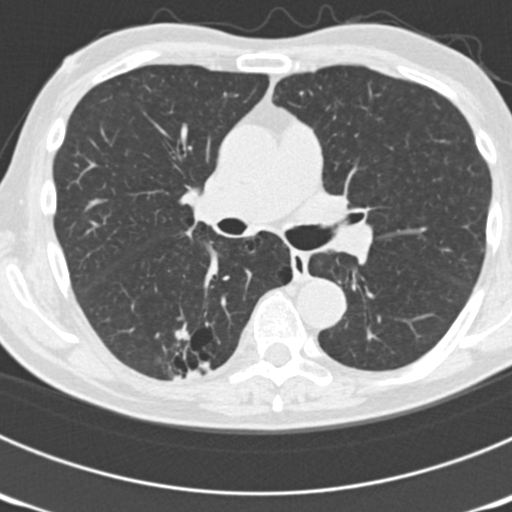
Low-dose screening chest CT, one axial slice. Slice 109 of 177 in the series (ordered by position). Reconstruction kernel B30f. 120 kVp. Lung window (W 1500 / L -600 HU). 2 mm slice thickness. 512 × 512 image matrix, field of view 300 × 300 mm.
Outlined on this slice (manually delineated by an expert):
- lesion 7 (nodule, lower lobe of right lung): bounding box [x1, y1, x2, y2] px = [173, 327, 190, 344]